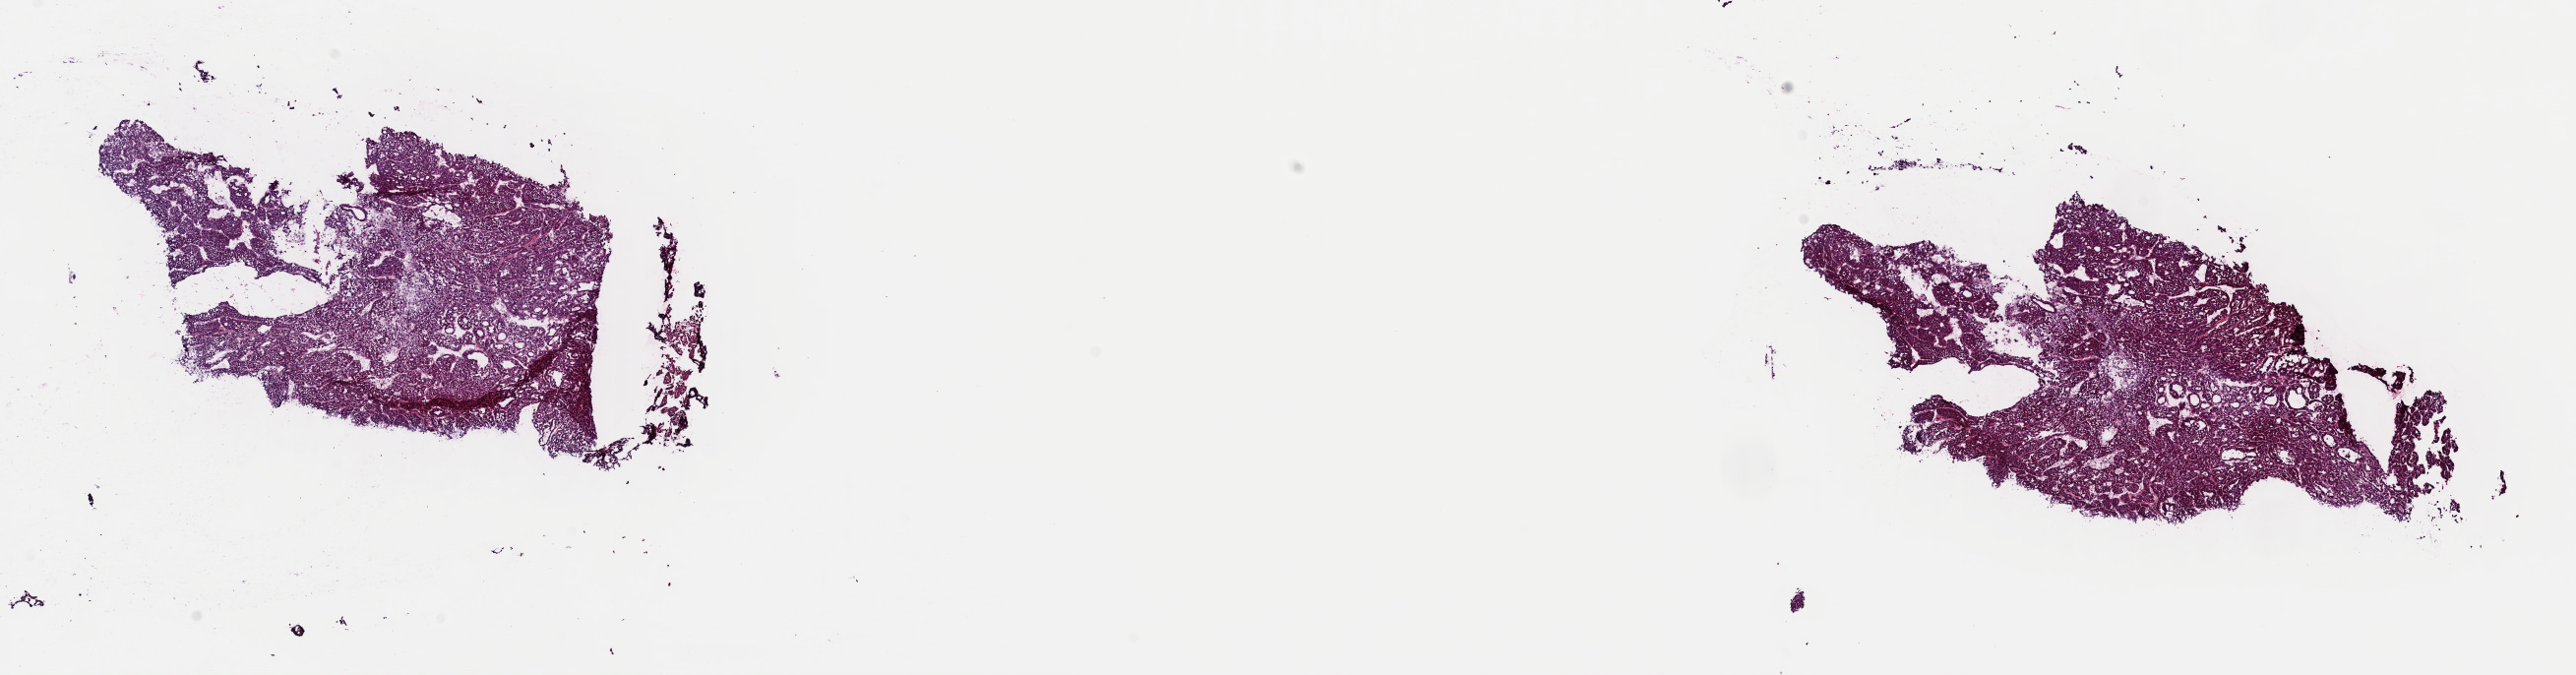
Whole-slide histology image, H&E-stained — a low-resolution overview of the entire scanned area, about 20.7 x 5.4 mm (from a 40x scan), frozen section from the top of the tissue portion, sample: primary tumour, liver. Male, age 66 years at initial diagnosis. Histologic grade: G1 (well differentiated). Slide review estimates, as recorded: tumour cells 88%, tumour nuclei 92%, normal cells 0%, stromal cells 6%, necrosis 6%. Inflammatory infiltration, as recorded: lymphocyte infiltration 2%, monocyte infiltration 1%, neutrophil infiltration 1%.
- pathologic diagnosis: Hepatocellular carcinoma, NOS
- AJCC pathologic stage: I (7th edition)
- TNM: T1 N0 M0